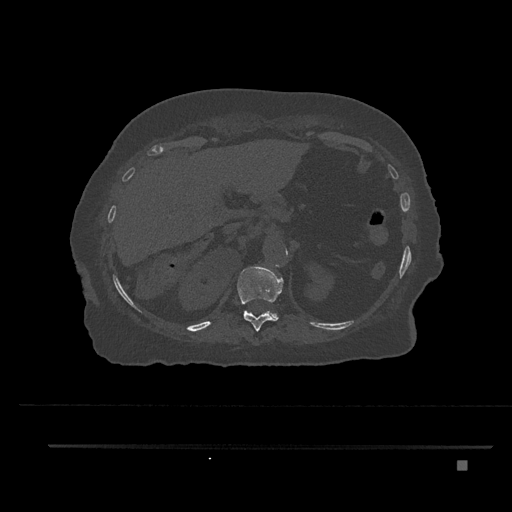
CT including the spine, one axial slice; position 305 of 797 along the scan axis; bone window (W 1800 / L 400 HU); 0.5 mm slice thickness; 512 × 512 image matrix, field of view 437 × 437 mm. Patient: female, 76 years. From the clinical record (not read from this slice): primary cancer: lung; vertebrae with lytic lesions (as recorded): T11, L3.
Annotated regions visible in this slice (semi-automatically segmented with operator editing):
- T11 vertebra: bounding box <237,266,283,332> (left, top, right, bottom; pixels)
- T12 vertebra: <263,312,278,318>